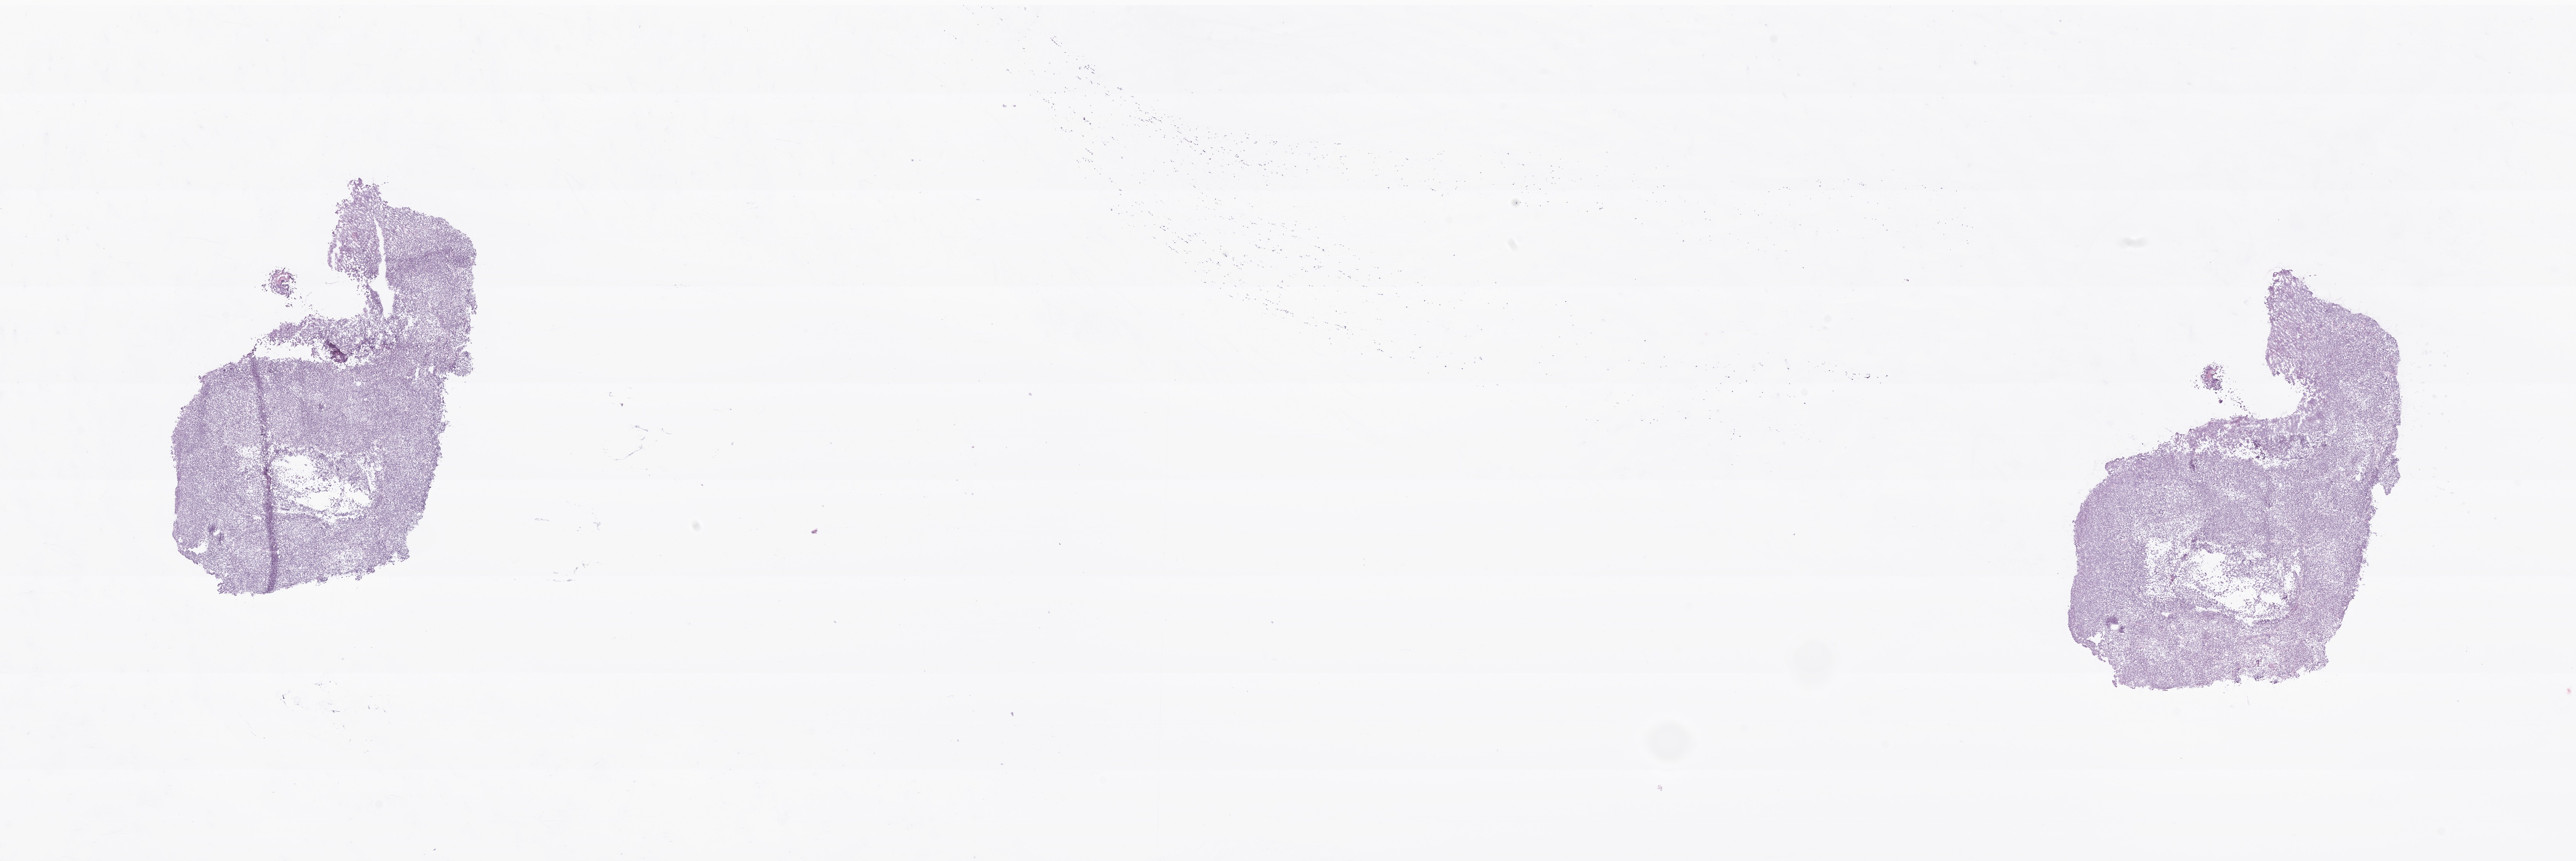
Whole-slide image, H&E stain of tumor tissue from the cerebellum — shown as a low-resolution overview of the whole scanned area (about 28.4 x 9.5 mm), frozen section (OCT-embedded). Patient: male, age 244 months (20 years 4 months).
Diagnosis: Medulloblastoma, NOS.